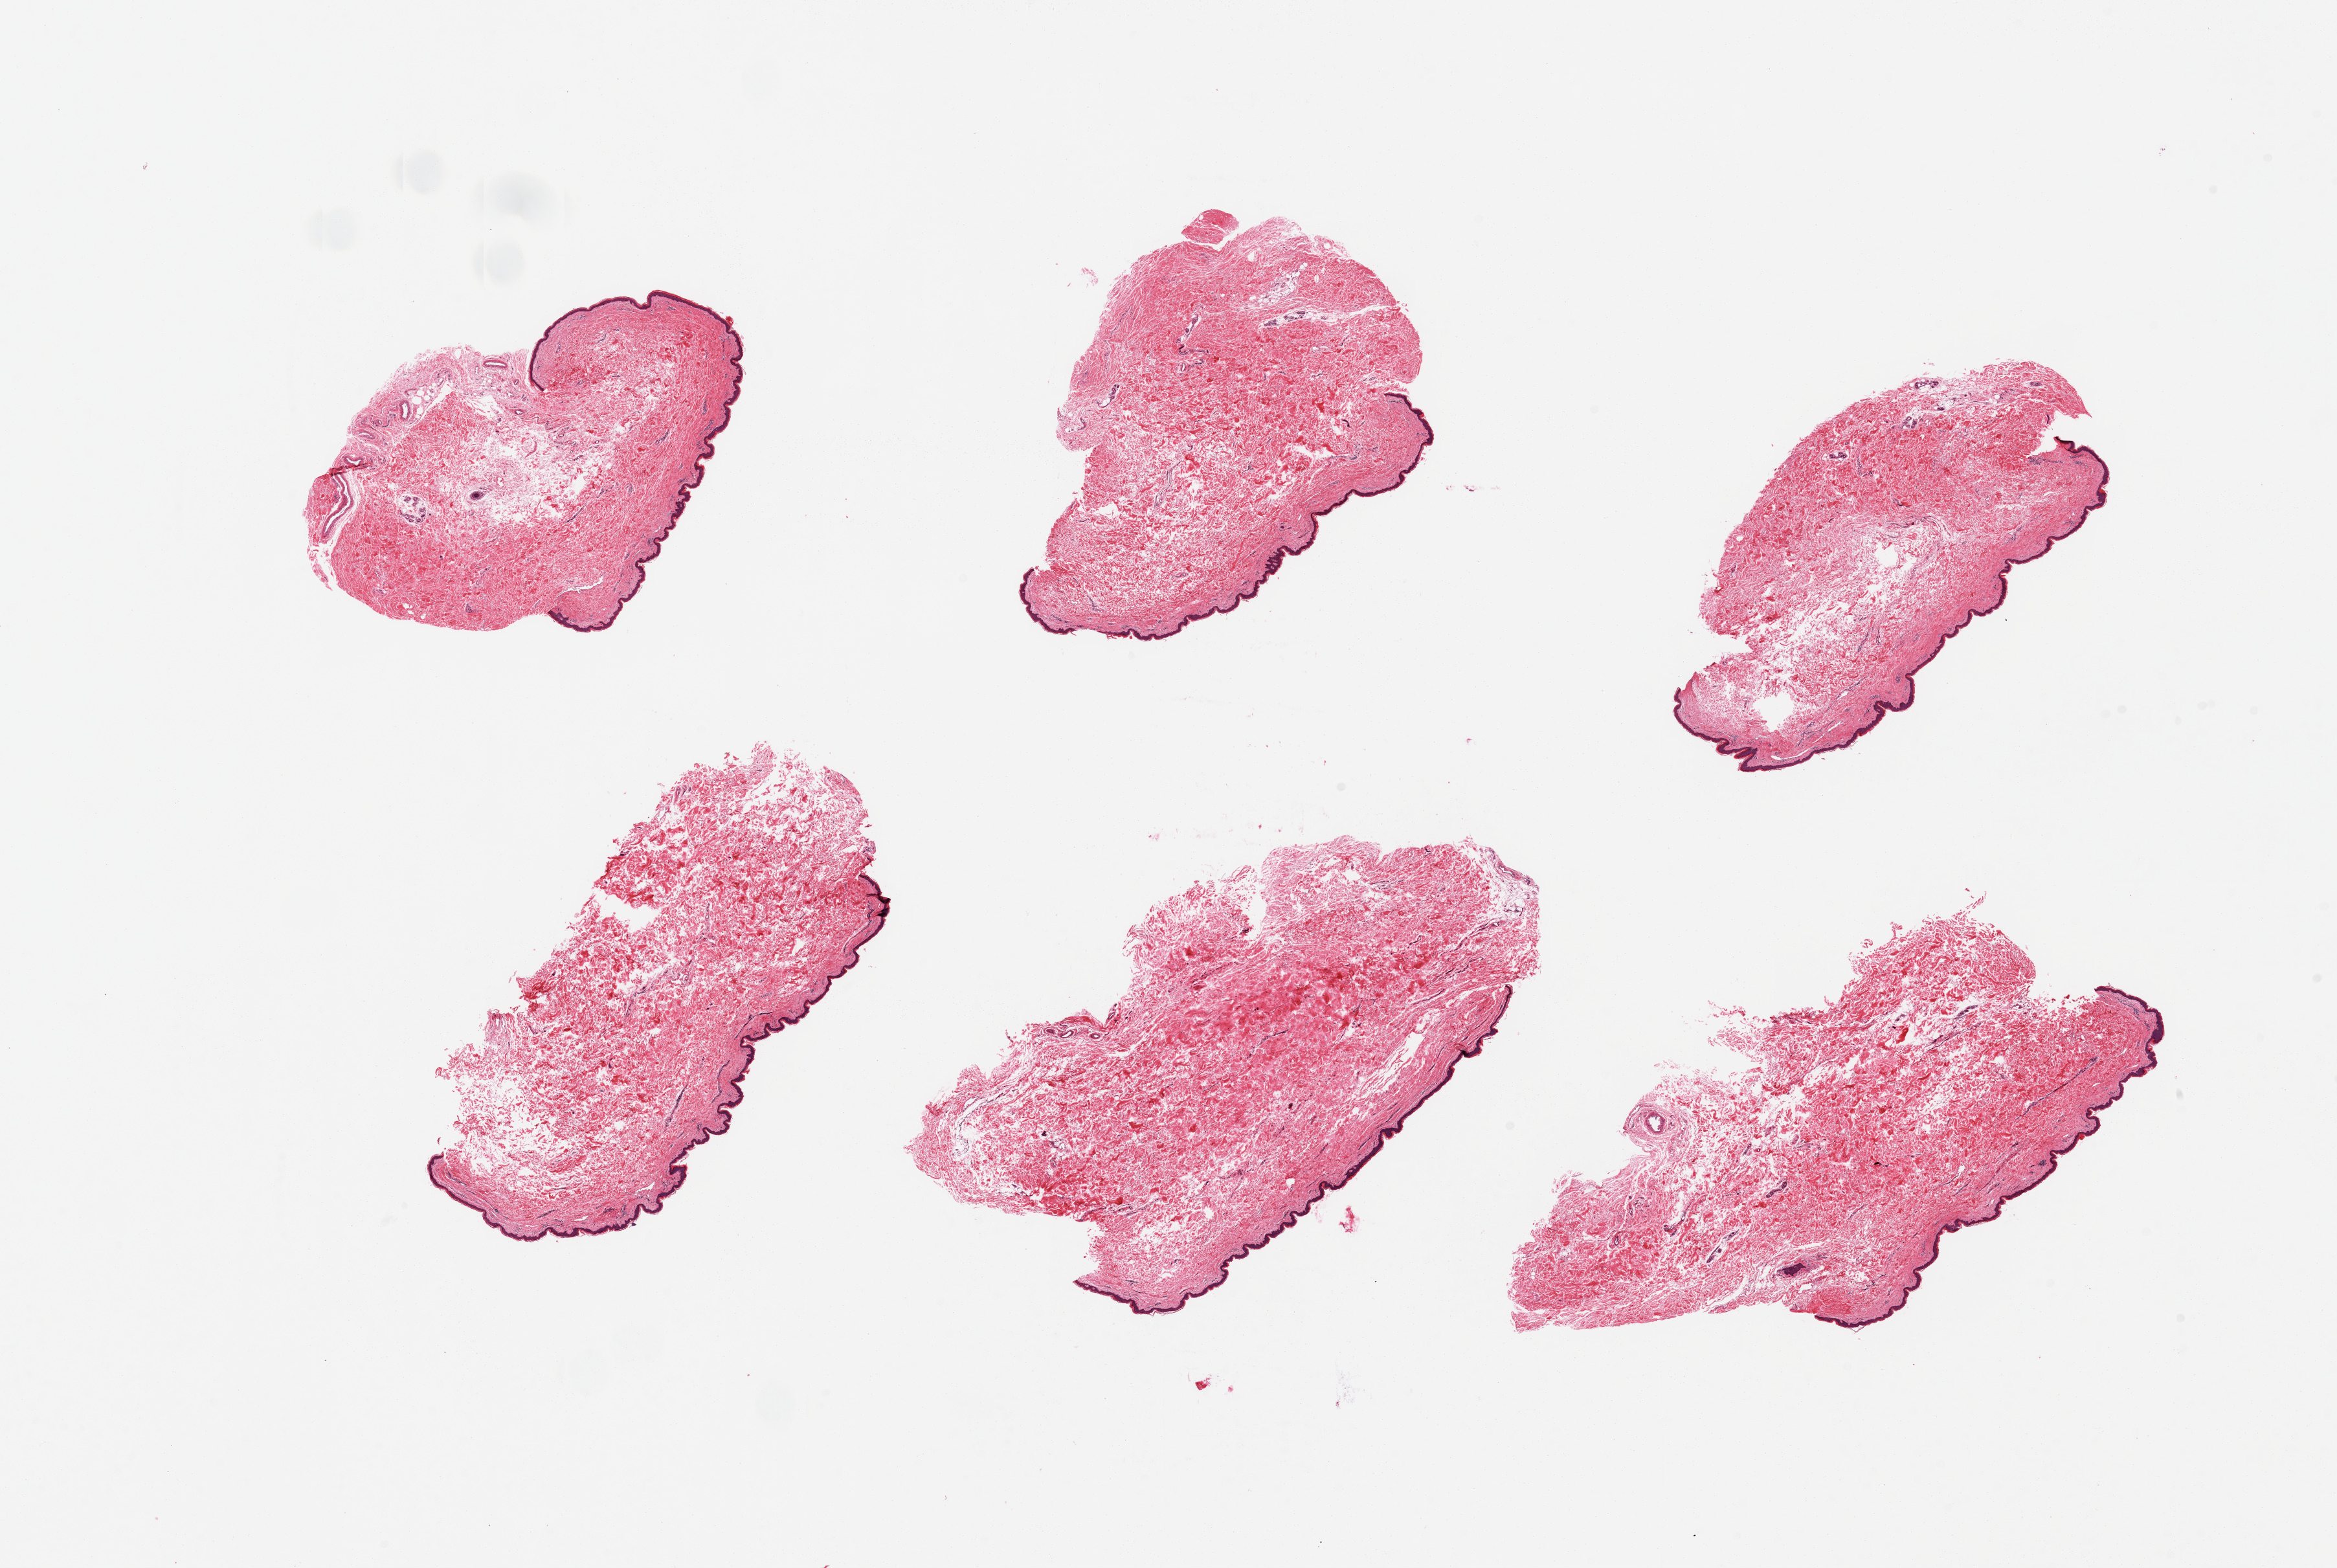
Whole-slide image, hematoxylin and eosin (H&E) stain, shown as a low-resolution overview of the whole scanned area (about 28.5 x 19.2 mm), PAXgene-fixed paraffin-embedded (PFPE) section, target tissue: skin of suprapubic region, donor tissue sample. Donor: female.
• pathologist's review note for this sample: 6 pieces, well trimmed